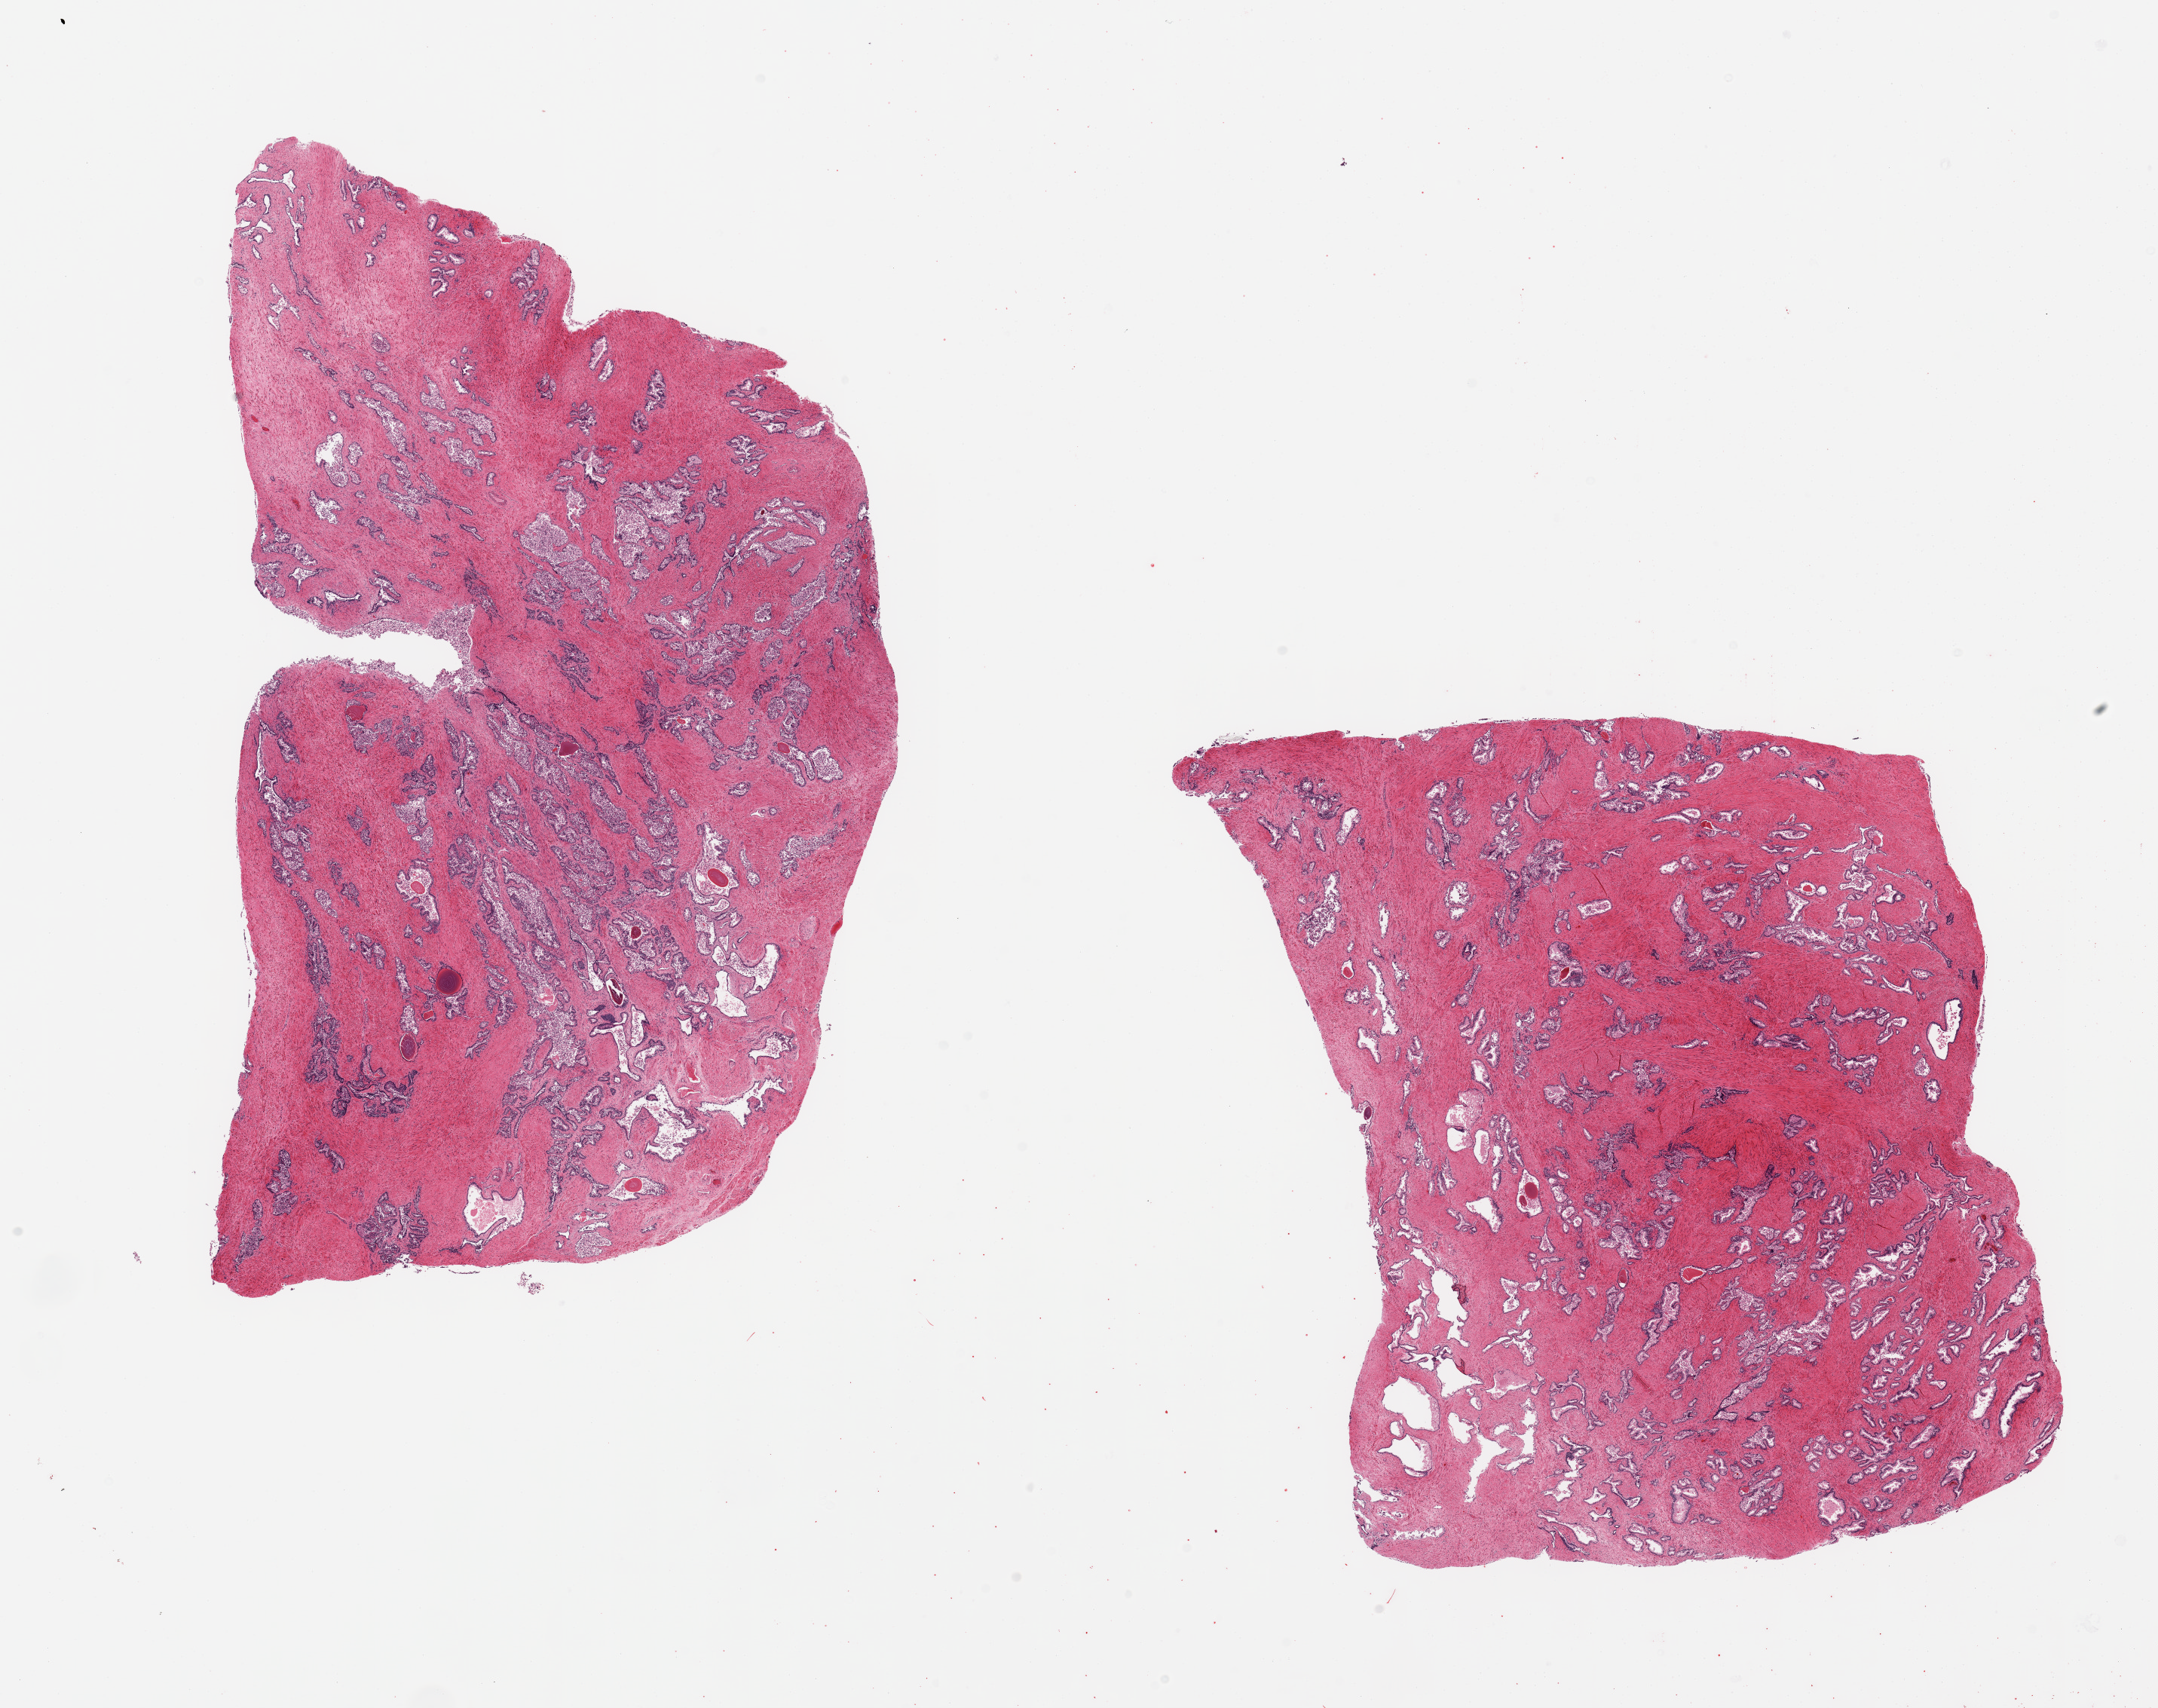
Whole-slide image, H&E stain — low-resolution overview of the scanned area, about 22.6 x 17.9 mm, PAXgene-fixed paraffin-embedded (PFPE) section, target tissue: prostate, tissue donor sample.
Reviewer comment on this tissue sample: 2 pieces, glandular mucosa with moderate-advanced autolysis.